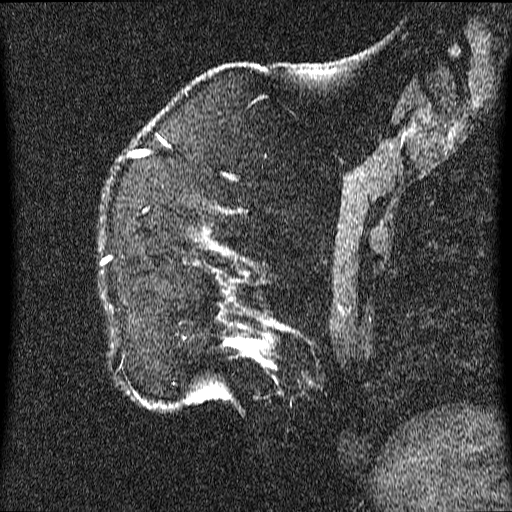
Breast MRI (dynamic contrast-enhanced), one sagittal slice; dynamic contrast-enhanced series, image 2 of 3 at this slice position (ordered by acquisition); 1.5 T; TE 4.2 ms, TR 9.1 ms; 2.2 mm slice thickness; 512 × 512 image matrix. Patient: female, 52 years.
Outlined on this slice (semi-automatically segmented with operator editing):
- analysis volume of interest (the breast-tissue region the enhancement analysis was run in; not a lesion): bounding box <101,205,349,410> (left, top, right, bottom; pixels)
- tumour enhancement mask (voxels above the 70 % enhancement threshold inside the analysis volume of interest): <224,340,268,365>